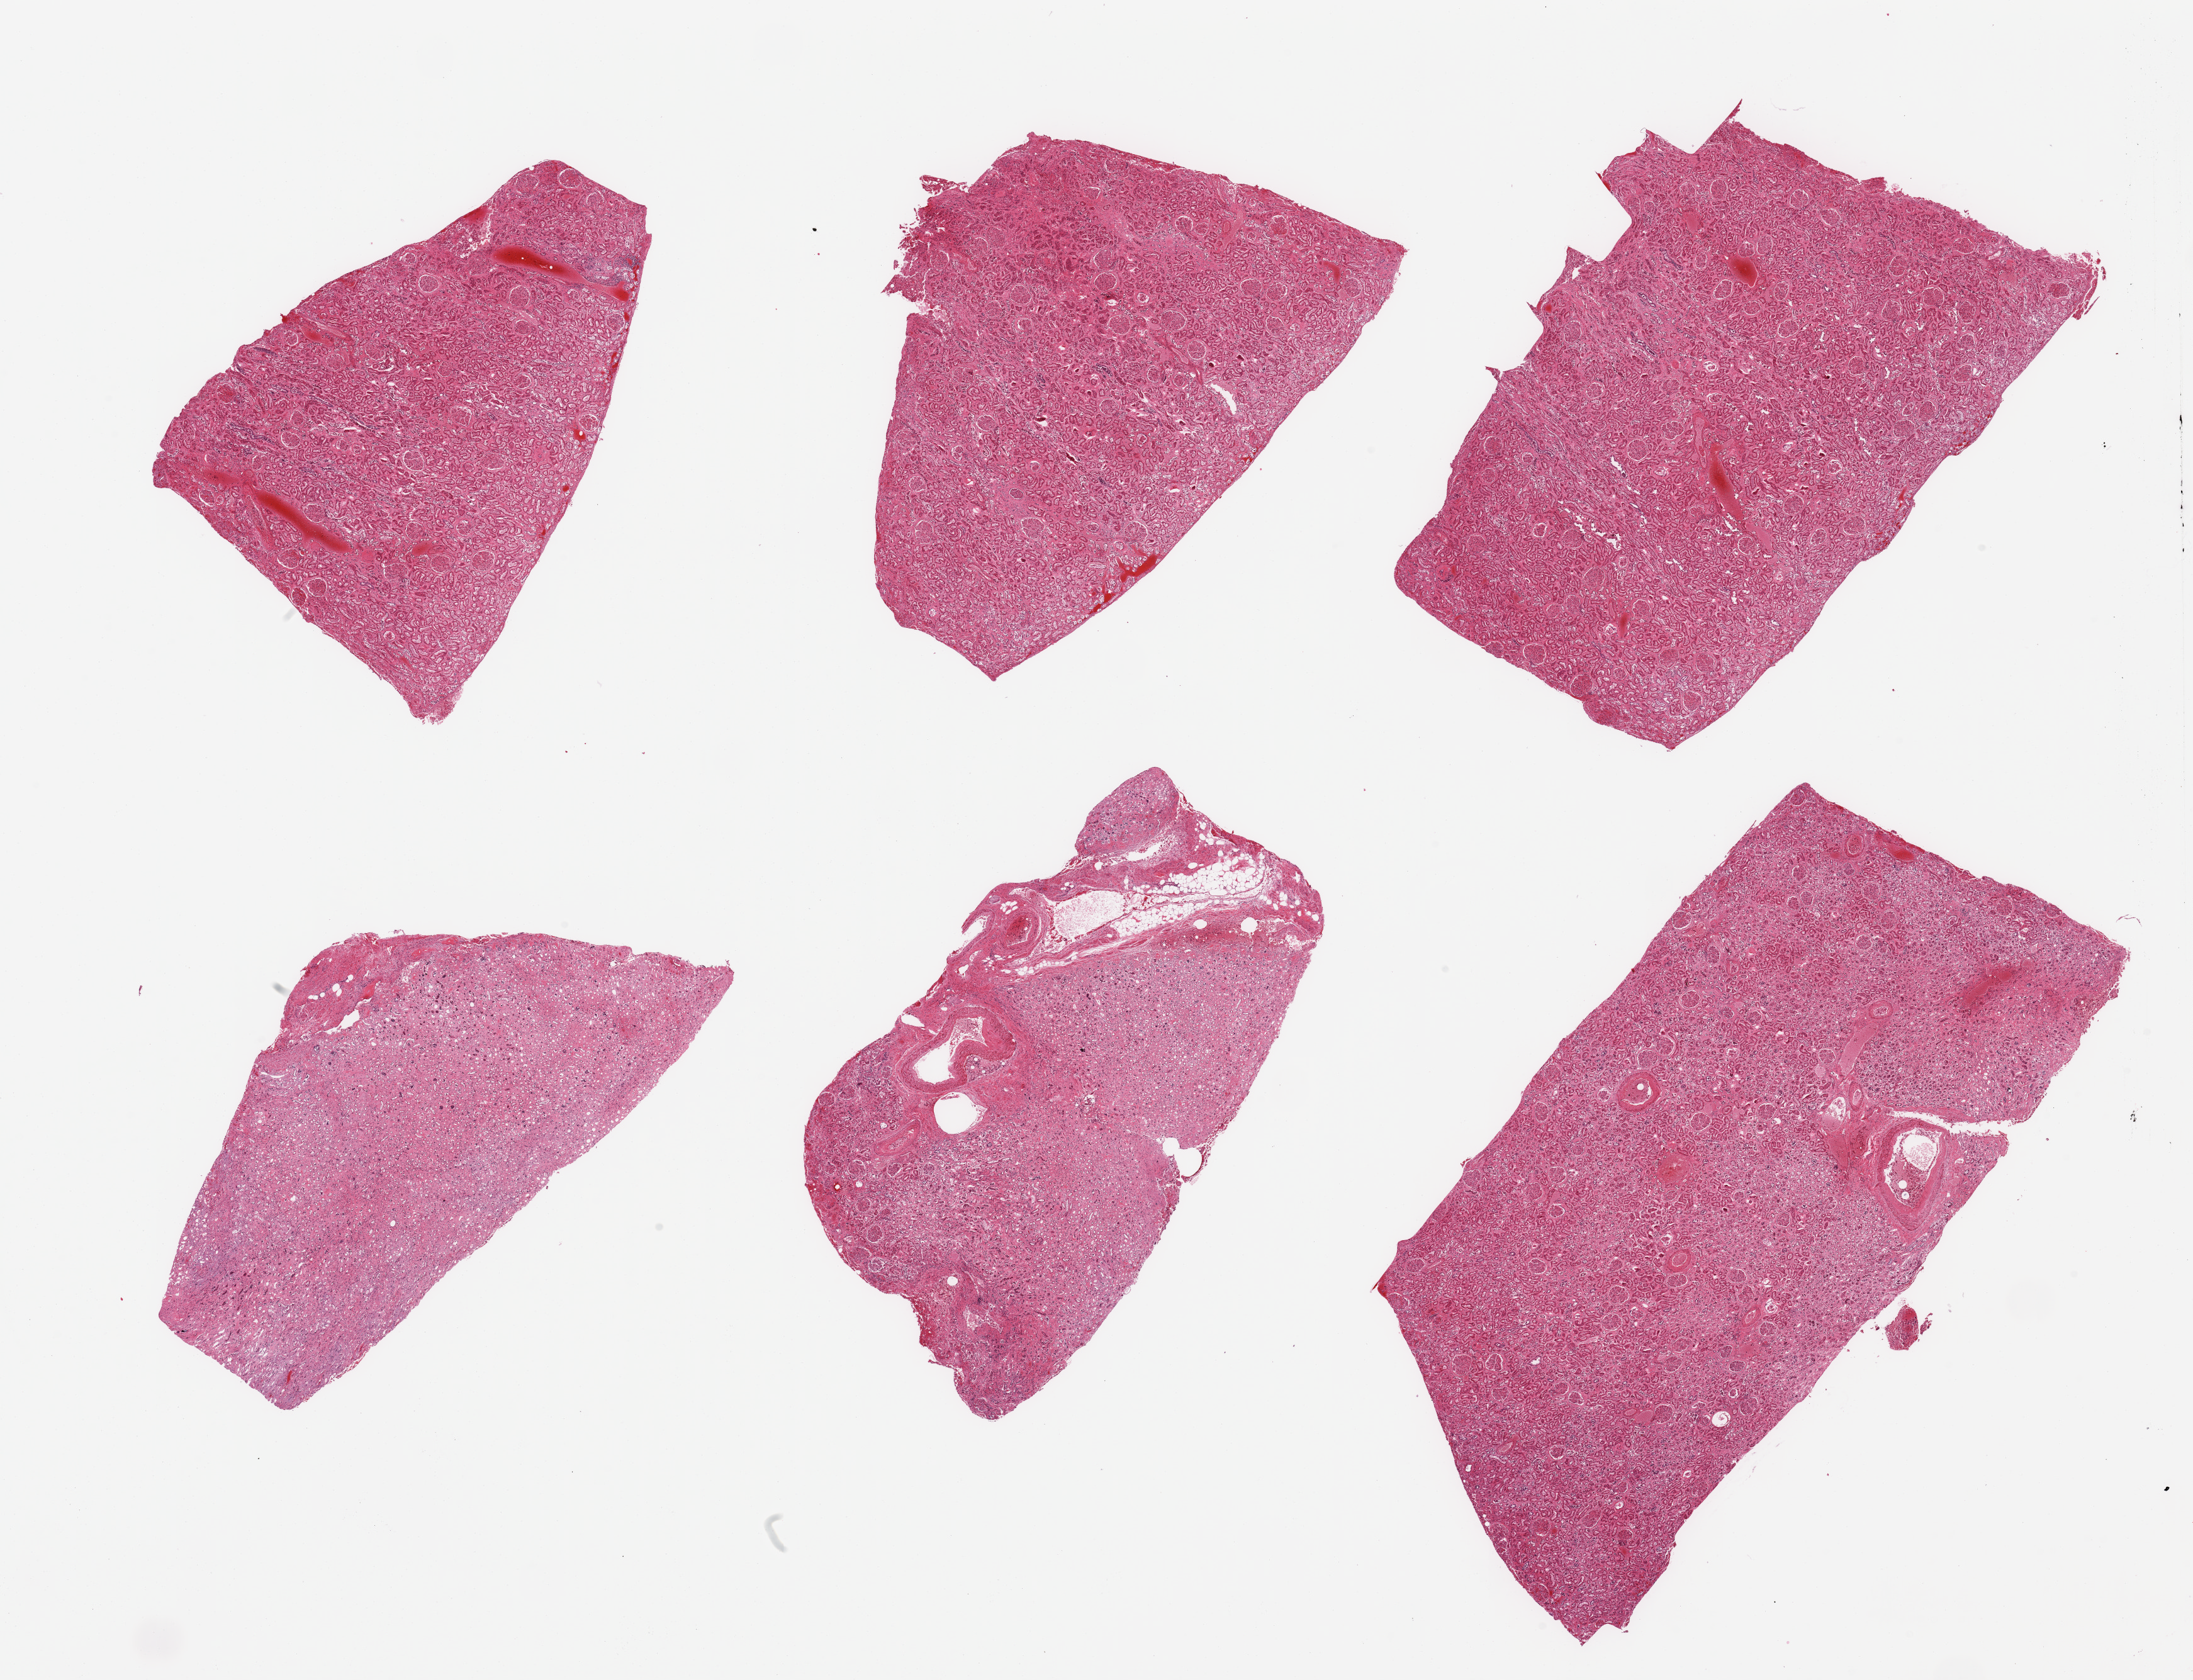
Digitized haematoxylin and eosin-stained section, a low-resolution overview of the entire scanned area, about 27.6 x 21.1 mm (slide scanned at 20x); PAXgene-fixed, paraffin-embedded tissue; section of renal cortex (target tissue); tissue donor sample. Female donor.
• reviewer comment on this tissue sample: 6 pieces; predominantly cortex, 2 are (largely) medulla, arteriosclerosis